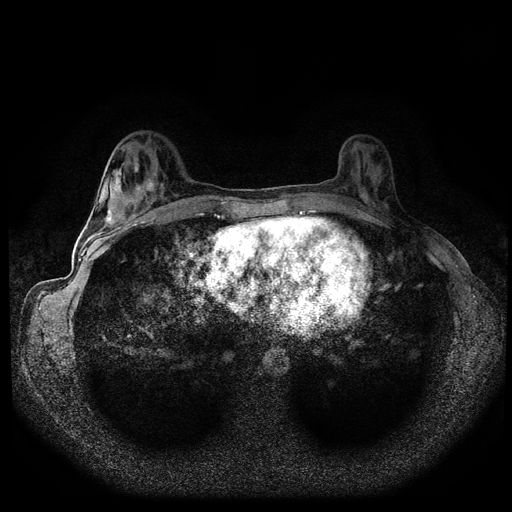
Breast MRI (dynamic contrast-enhanced, multi-phase), one axial slice; slice 35 of 108 in the series (ordered by position); dynamic contrast-enhanced series, time point 2 of 5 at this slice position (early post-contrast); 1.5 T; TE 2.7 ms, TR 5.5 ms; 512 × 512 image matrix. Patient: female, 36 years.
Annotated regions visible in this slice (semi-automatically segmented with operator editing):
- breast lesion (labelled benign in the annotation): bounding box <143,175,157,195> (left, top, right, bottom; pixels)
- breast lesion (labelled benign in the annotation): <107,167,128,199>
- breast lesion (labelled benign in the annotation): <103,207,118,230>